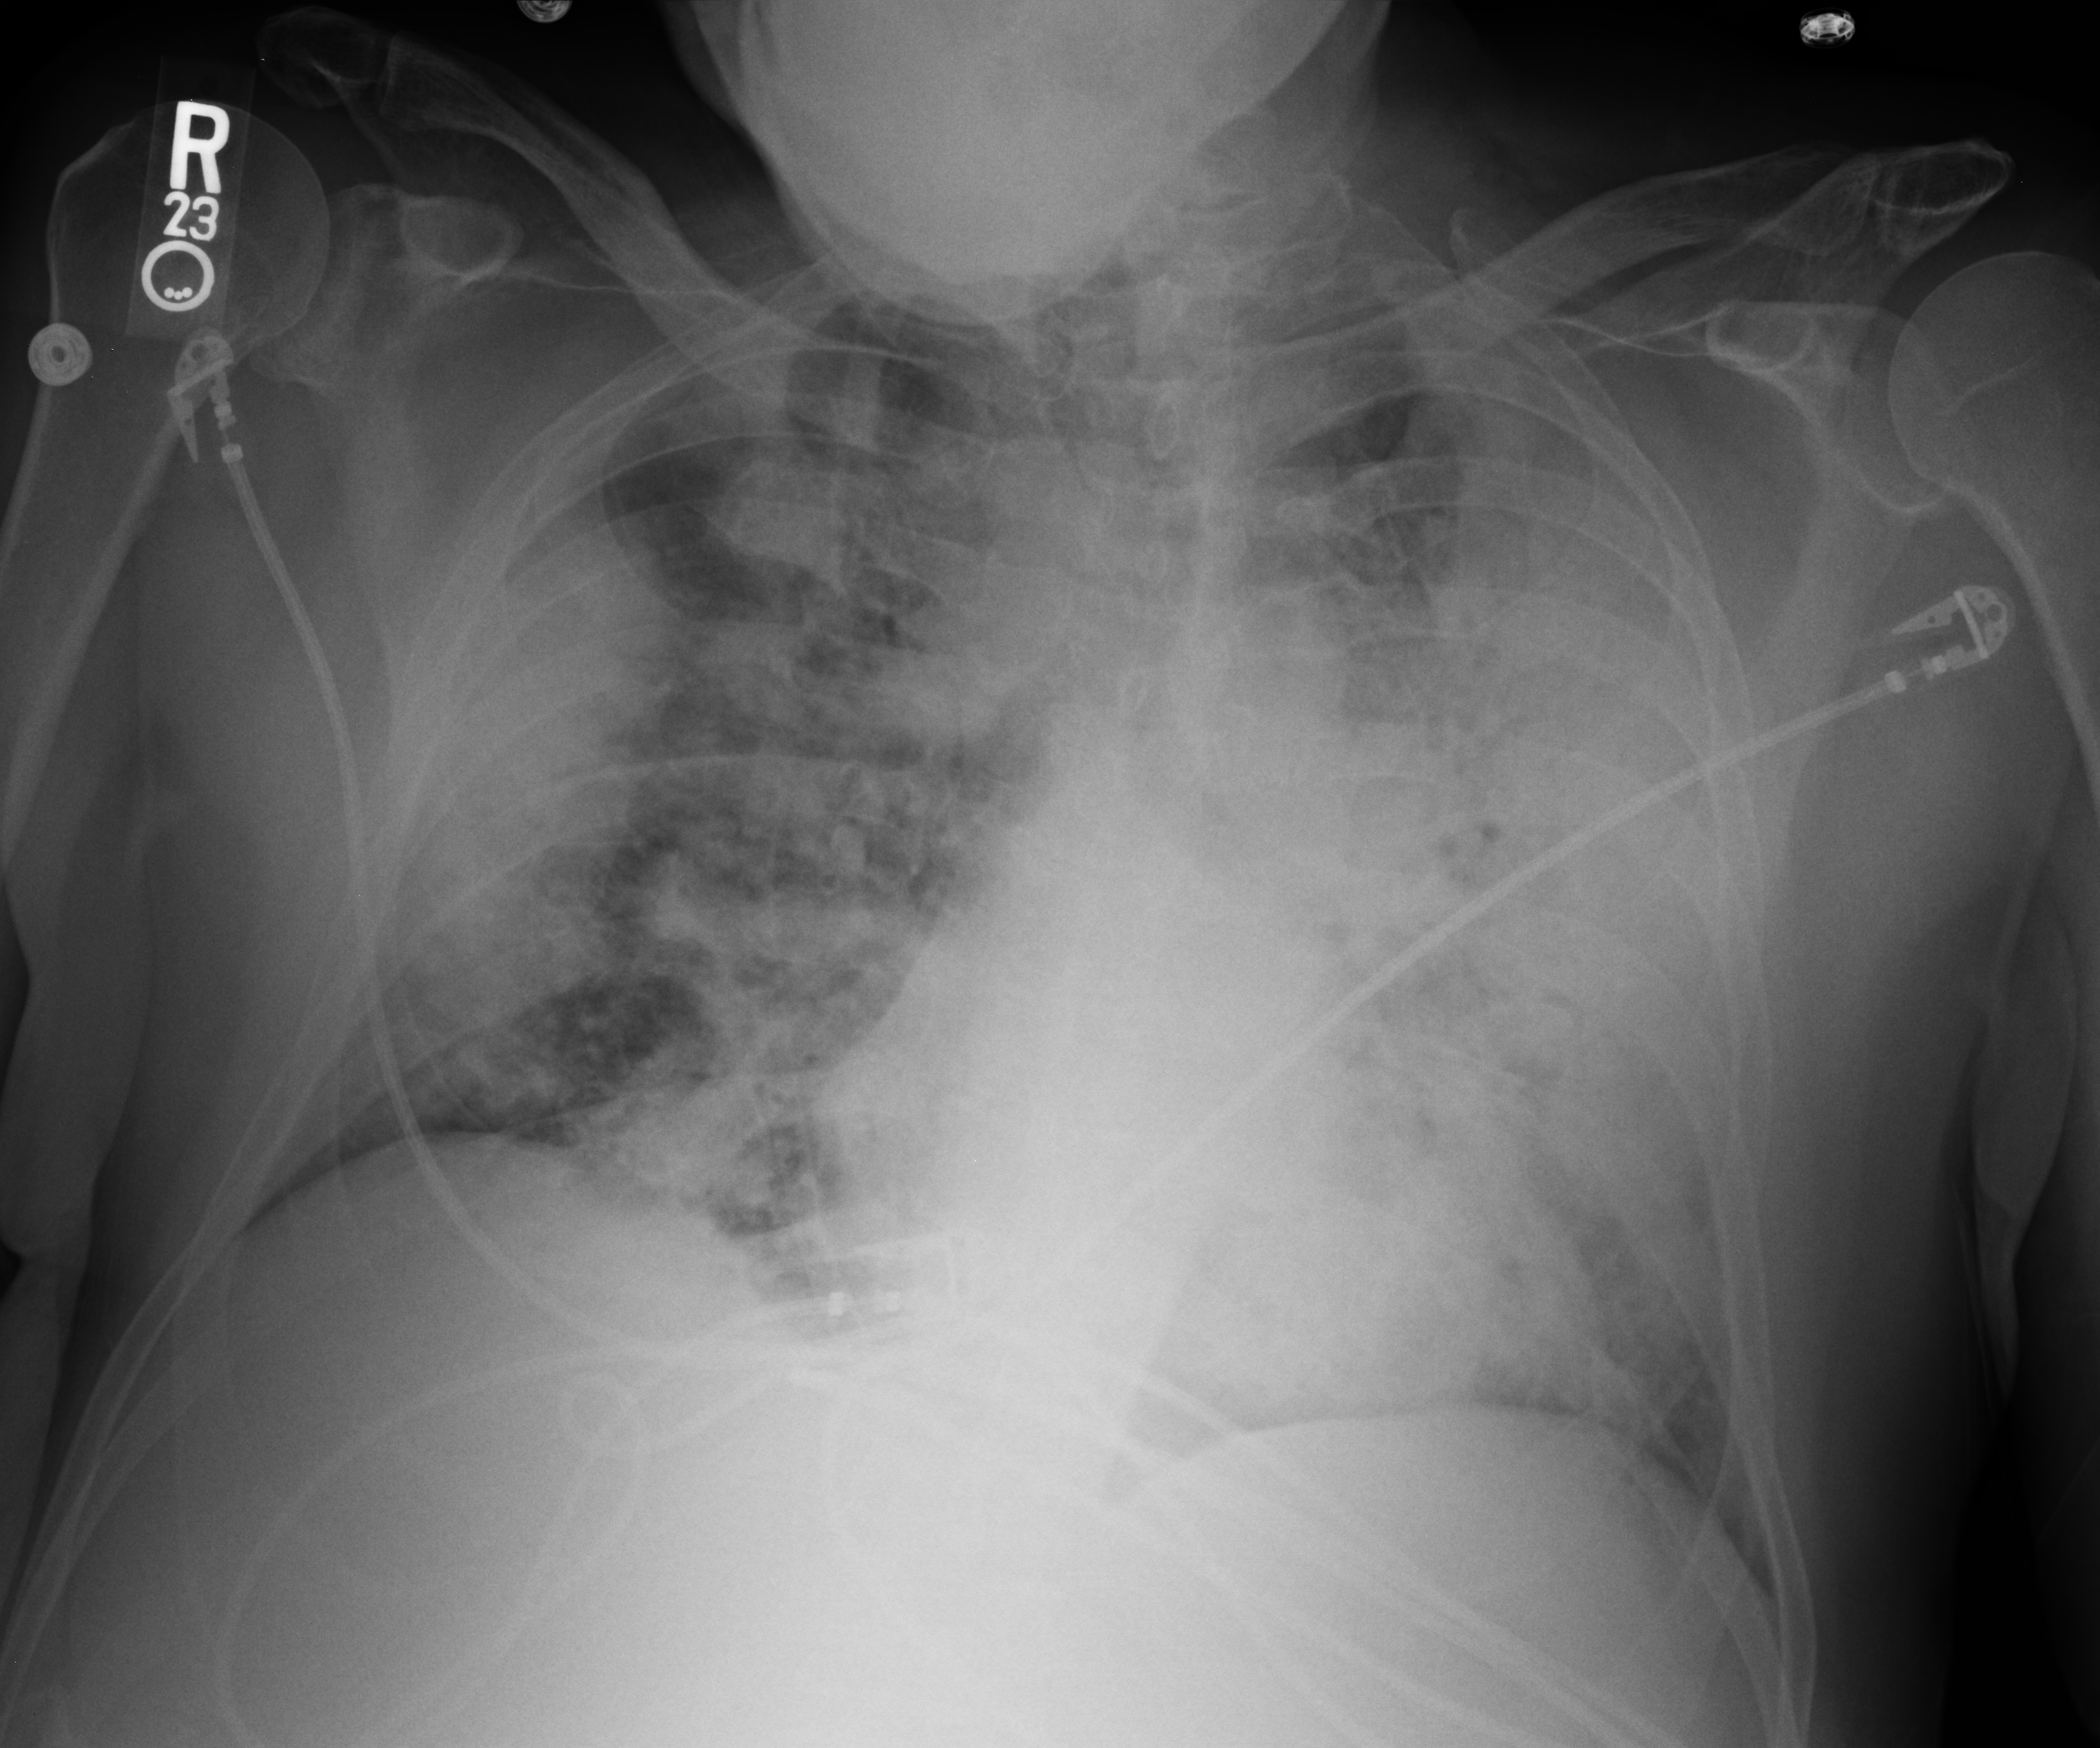
Bedside chest radiograph (computed radiography); anteroposterior (AP) projection. Patient hospitalised with COVID-19; male, aged 18–59 years.
Admission-level facts for this patient (not findings on this image; timing relative to this image not recorded): length of hospital stay: 25 days; hypertension (admission record): yes.